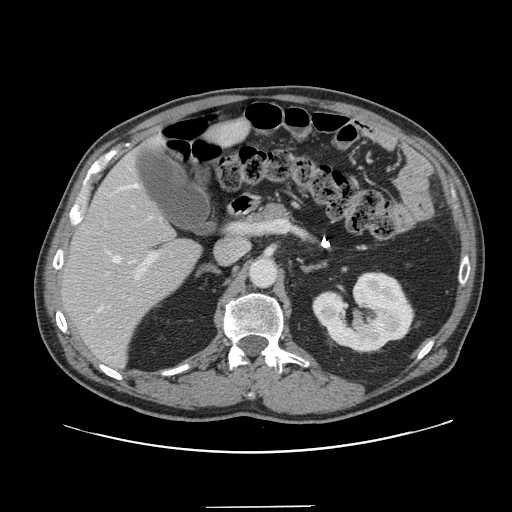
Contrast-enhanced abdominal CT, one axial slice; slice 81 of 139 in the series (ordered by position); soft-tissue window (W 400 / L 40 HU); 2.5 mm slice thickness; 512 × 512 image matrix. Male patient, age 64 years. Case-level facts recorded for this patient, not image findings: diagnosis: colorectal cancer liver metastases, imaged before liver resection; multiple liver metastases: yes; largest metastasis: 3.5 cm.
Outlined on this slice (manually delineated by an expert):
- hepatic veins: bounding box (x1, y1, x2, y2) in pixels: (98, 184, 161, 312)
- liver: (63, 123, 245, 367)
- planned liver remnant (the part of the liver to remain after resection): (62, 123, 245, 366)
- portal vein (with intrahepatic branches): (135, 253, 156, 279)